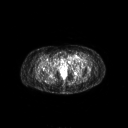
FDG PET of an extremity soft-tissue mass (from a PET/CT study), one axial slice. Position 49 of 267 along the scan axis. 128 × 128 image matrix, field of view 700 × 700 mm. Female patient, age 47 years. From the clinical record (not read from this slice): histological type: myxofibrosarcoma; grade: intermediate; site of the primary tumour: left thigh.
Annotated regions visible in this slice (expert contour drawn on MRI and transferred to this co-registered scan by the dataset authors):
- gross tumour volume including surrounding oedema: box from (x=66, y=55) to (x=83, y=63) px